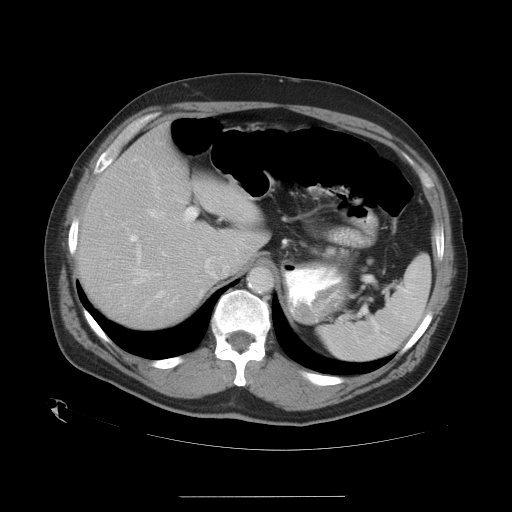
Contrast-enhanced abdominal CT, one axial slice; position 23 of 35 along the scan axis; reconstruction kernel STANDARD; 120 kVp; intravenous contrast given; soft-tissue window (W 400 / L 40 HU); 7.5 mm slice thickness; 512 × 512 image matrix, field of view 450 × 450 mm. Male patient, age 67 years. Case-level facts recorded for this patient, not image findings: diagnosis: colorectal cancer liver metastases, imaged before liver resection; multiple liver metastases: no; largest metastasis: 2.3 cm; disease in both lobes: no.
Outlined on this slice (expert manual segmentation):
- hepatic veins: bounding box (x1, y1, x2, y2) in pixels: (139, 209, 163, 298)
- liver: (79, 127, 262, 329)
- planned liver remnant (the part of the liver to remain after resection): (85, 127, 262, 329)
- portal vein (with intrahepatic branches): (129, 207, 196, 284)